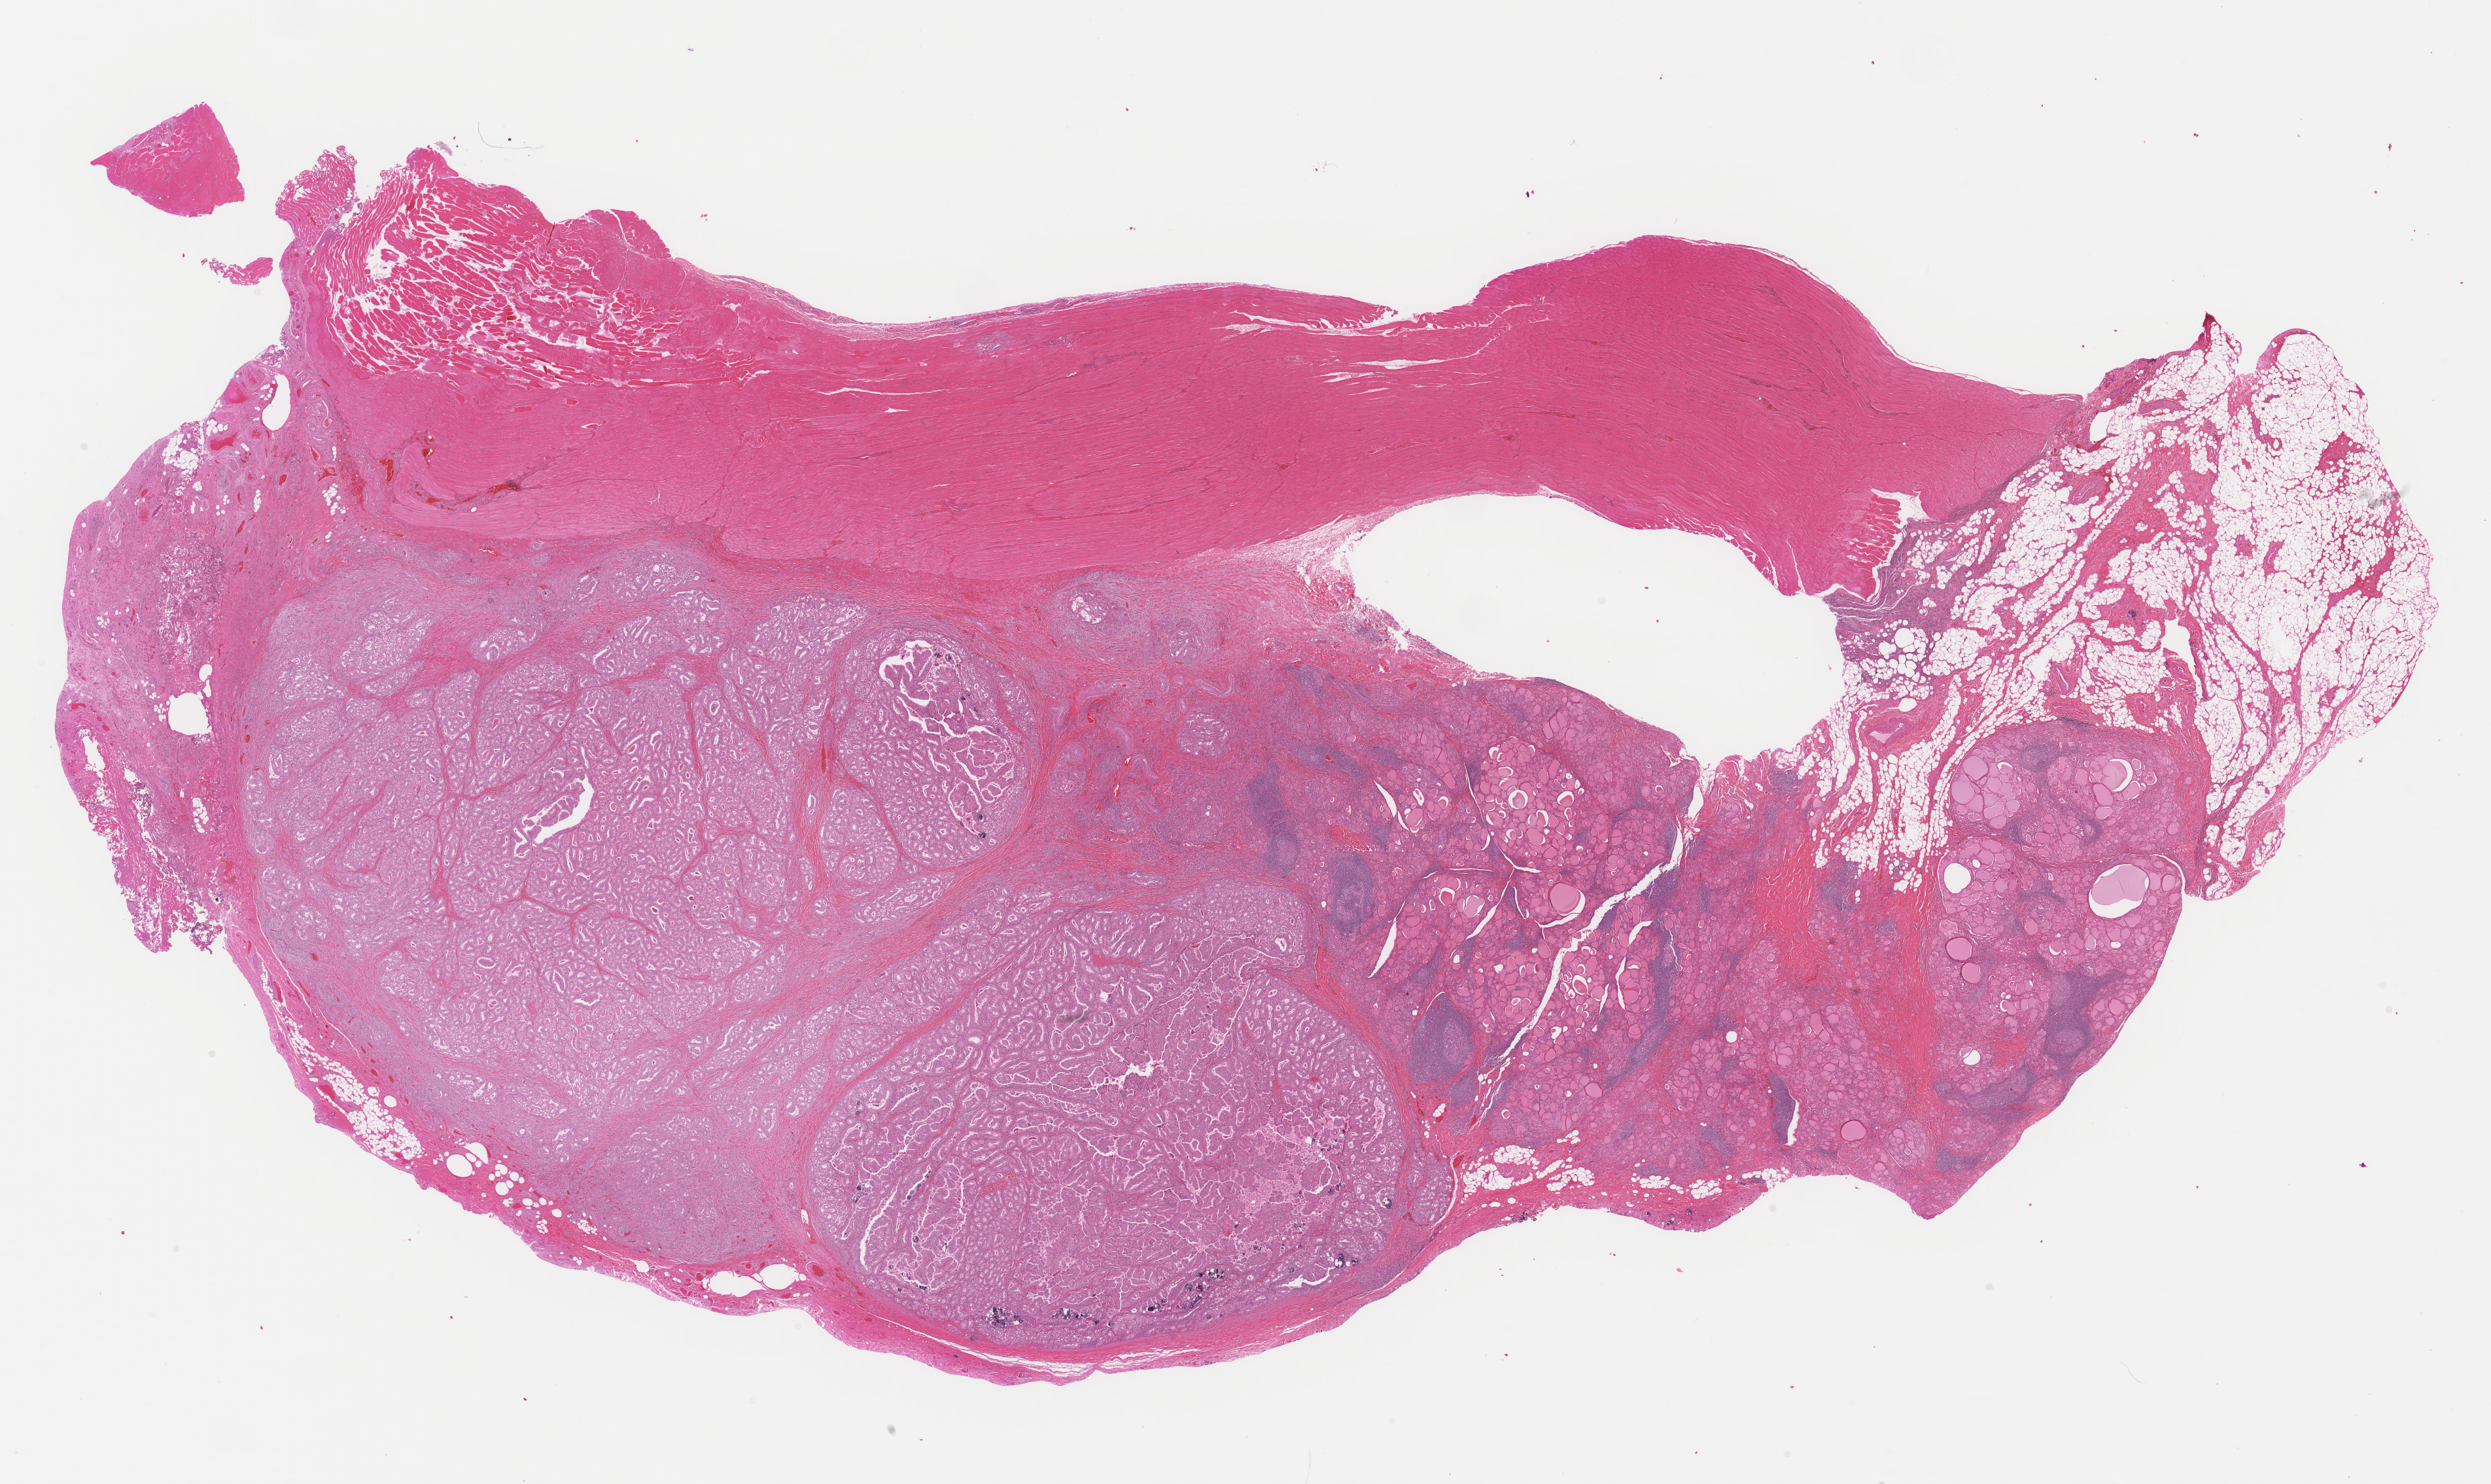
Digitized H&E tissue section (whole slide) — shown as a low-resolution overview of the whole scanned area (about 30.0 x 17.9 mm); formalin-fixed paraffin-embedded (FFPE) diagnostic section; sample: primary tumour, thyroid. Female patient; age at initial diagnosis 55 years.
Pathologic diagnosis: Papillary adenocarcinoma, NOS (thyroid gland). AJCC pathologic stage: III (6th edition). Lymph nodes positive (case pathology): 6 of 23 examined. Laterality: midline.